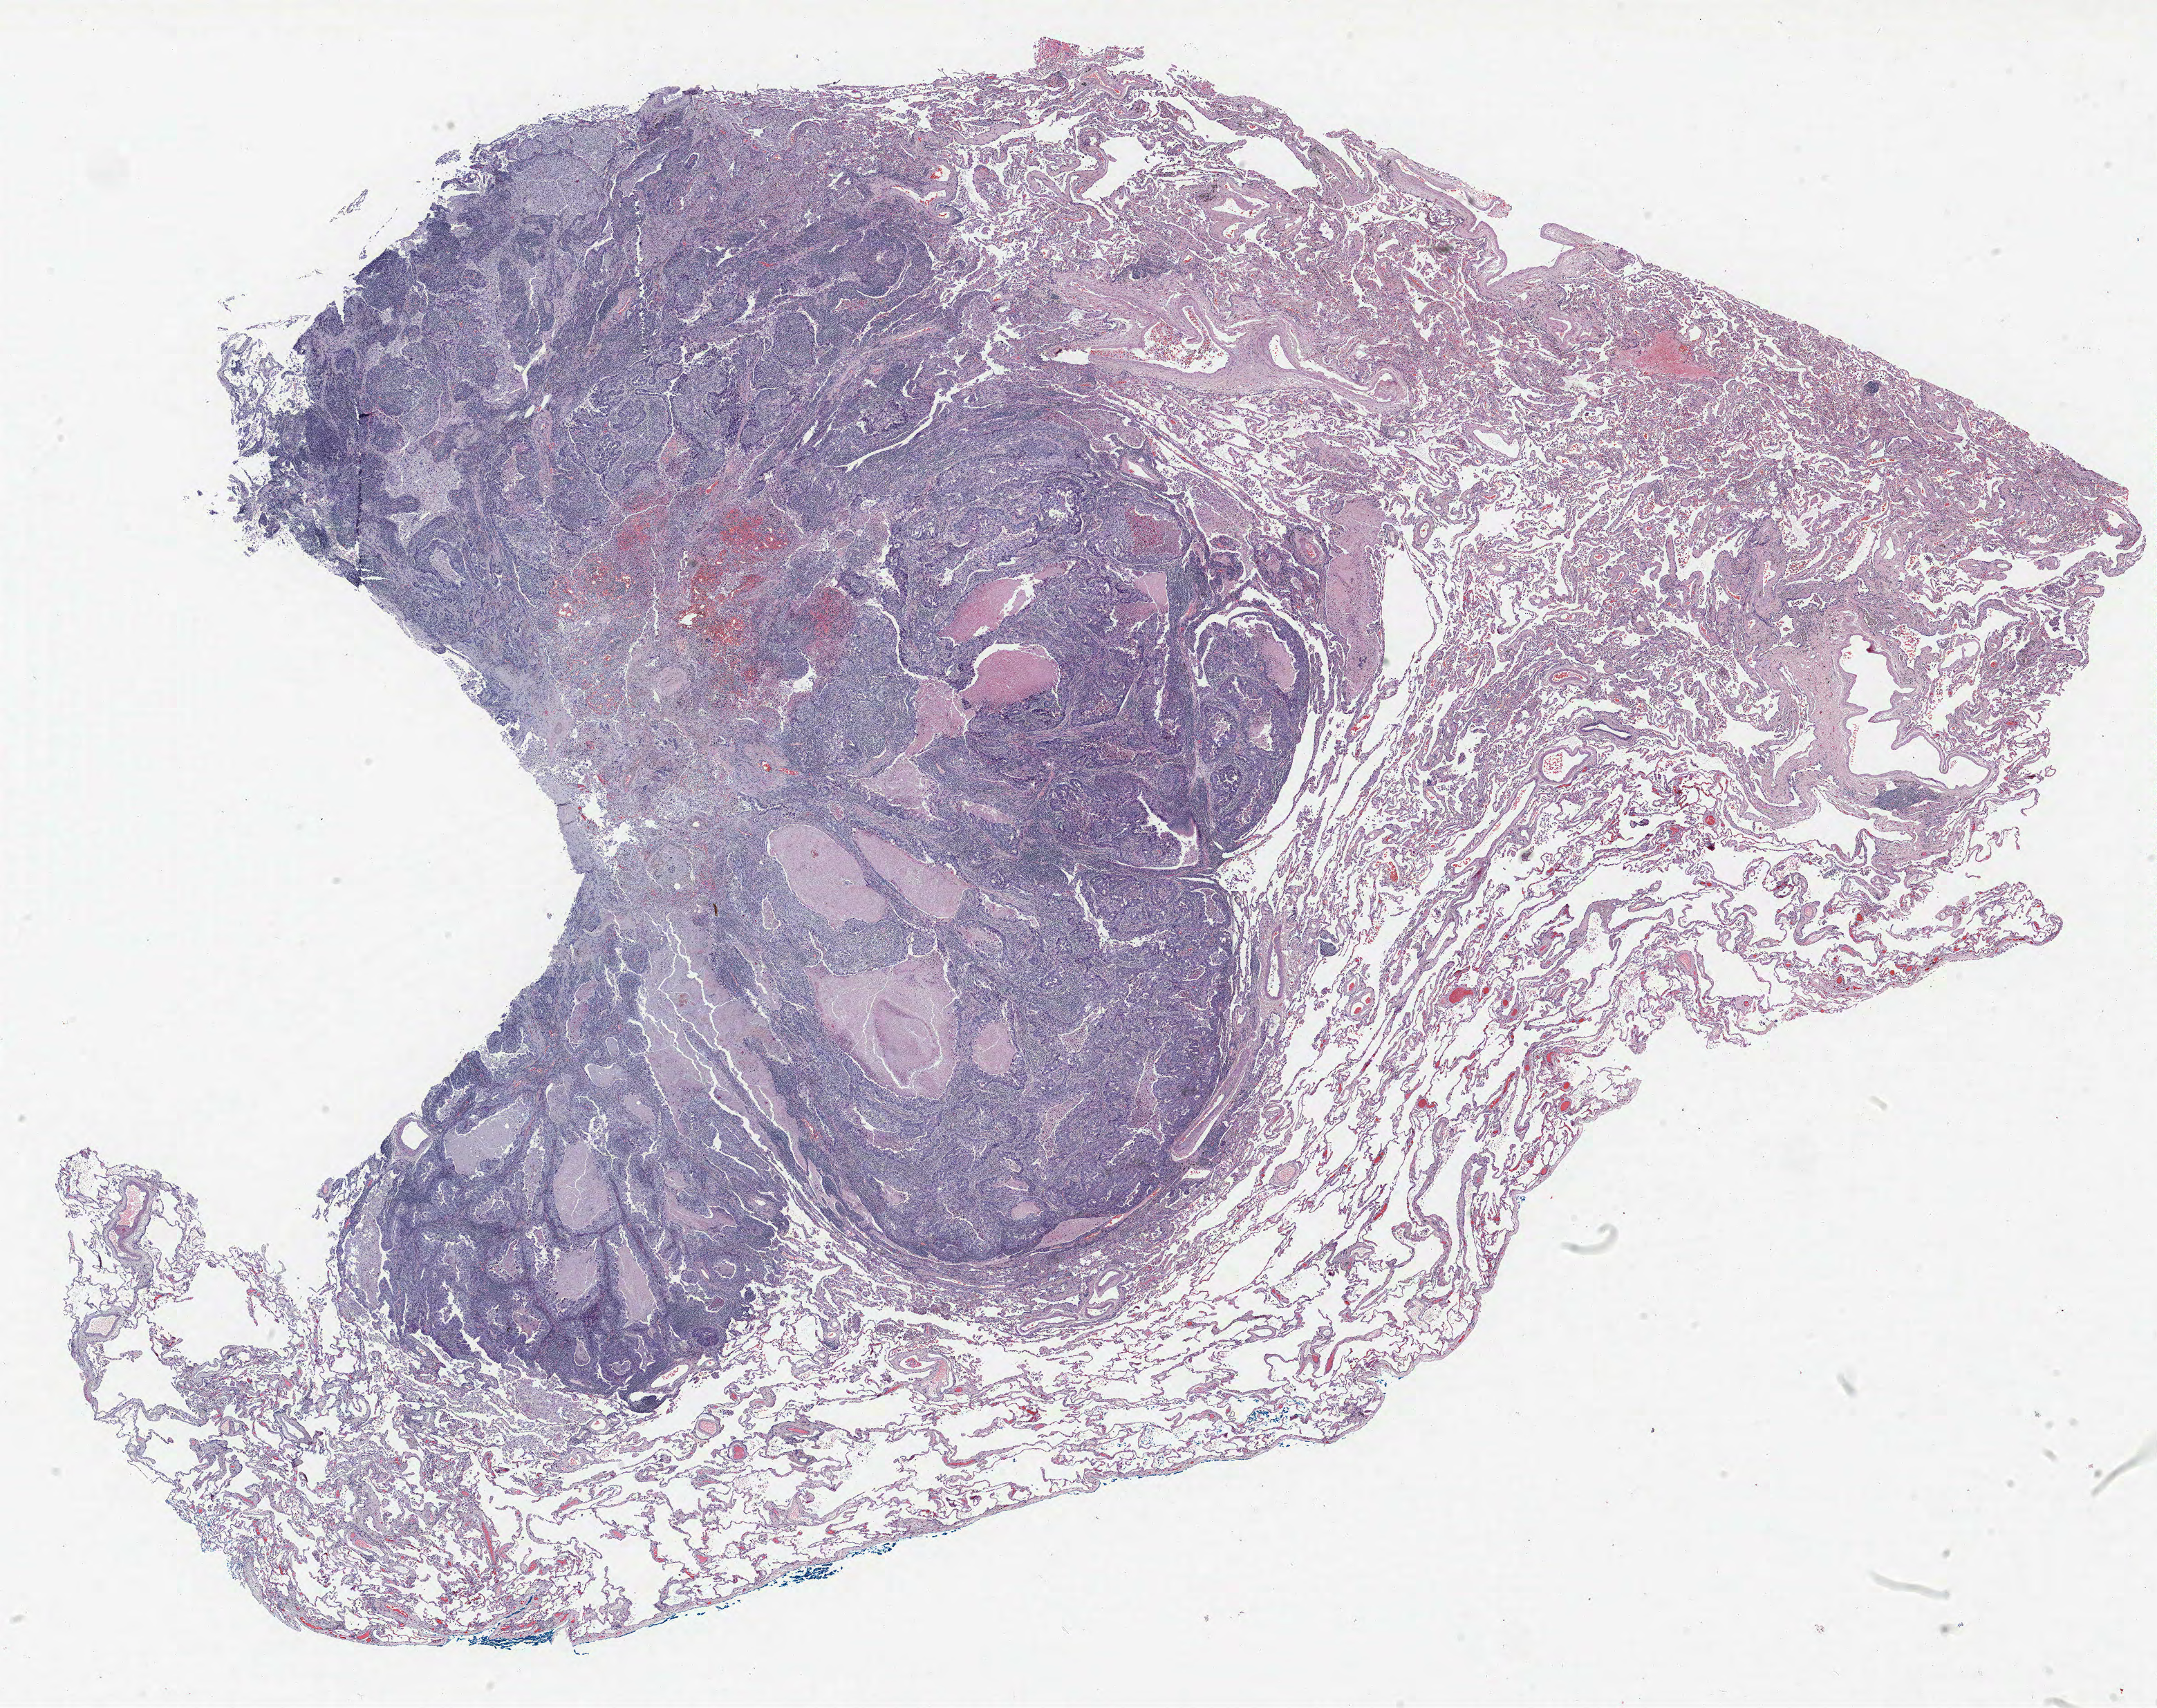
Whole-slide histology image, H&E-stained, whole scanned area (about 25.0 x 19.8 mm) shown as a low-resolution overview, FFPE section, lung. Female patient, aged 61 at enrolment. Current smoker at enrolment. Grade: moderately differentiated (G2).
- tumour size (pathology): 18 mm
- stage (AJCC 6th edition): IA
- ICD-O-3 topography: lower lobe of lung (C34.3)
- primary tumour location (clinical record): left lower lobe
- participant's lung-cancer diagnosis: Adenocarcinoma, NOS (ICD-O-3 8140/3)